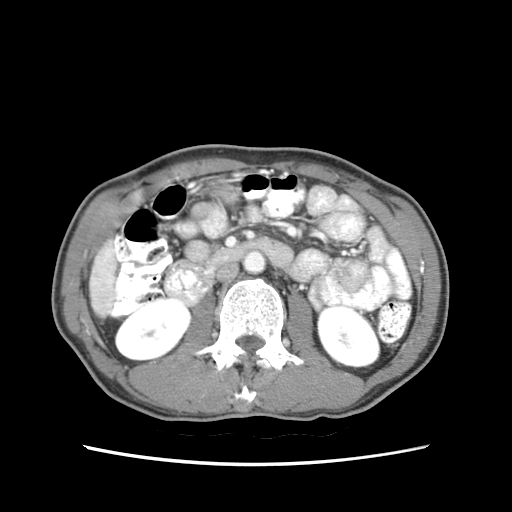
Contrast-enhanced abdominal CT (liver protocol), one axial slice. Slice 12 of 79 in the series (ordered by position). Reconstruction kernel STANDARD. Soft-tissue window (W 400 / L 40 HU). 2.5 mm slice thickness. 512 × 512 image matrix. Case-level facts recorded for this patient, not image findings: diagnosis: hepatocellular carcinoma (patient treated with transarterial chemoembolisation; whether this scan precedes or follows treatment is not stated here); TNM stage (as recorded): Stage-IIIB; Child-Pugh class: A; tumour differentiation: moderately differentiated; tumour nodularity: multinodular.
Annotated regions visible in this slice (semi-automatically segmented with operator editing):
- liver parenchyma outside the tumour (the mass and vessels are separate outlines, so this box may not span the whole liver): bounding box [x1, y1, x2, y2] px = [90, 239, 116, 314]
- liver vessels: [110, 267, 113, 273]